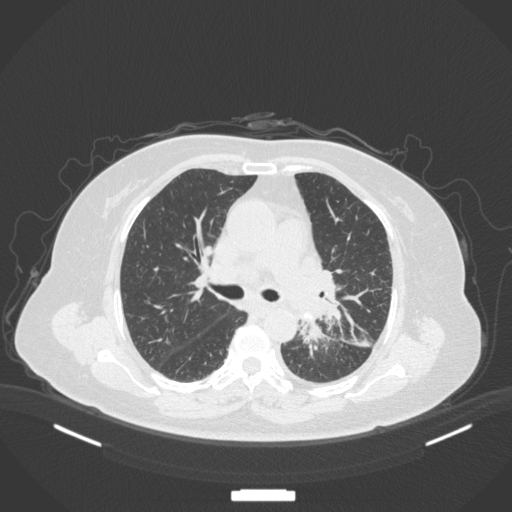
Chest CT, one axial slice. Position 217 of 328 along the scan axis. Reconstruction kernel B31f. 120 kVp. Lung window (W 1500 / L -600 HU). 1 mm slice thickness. 512 × 512 image matrix. Female patient, age 69 years. Case-level facts recorded for this patient, not image findings: clinical TNM (as recorded): T2b N3 M1.
Structures marked on this image (rectangle marked by the reading radiologist):
- lung tumour (recorded histology: adenocarcinoma): bounding box [x1, y1, x2, y2] px = [297, 313, 329, 356]